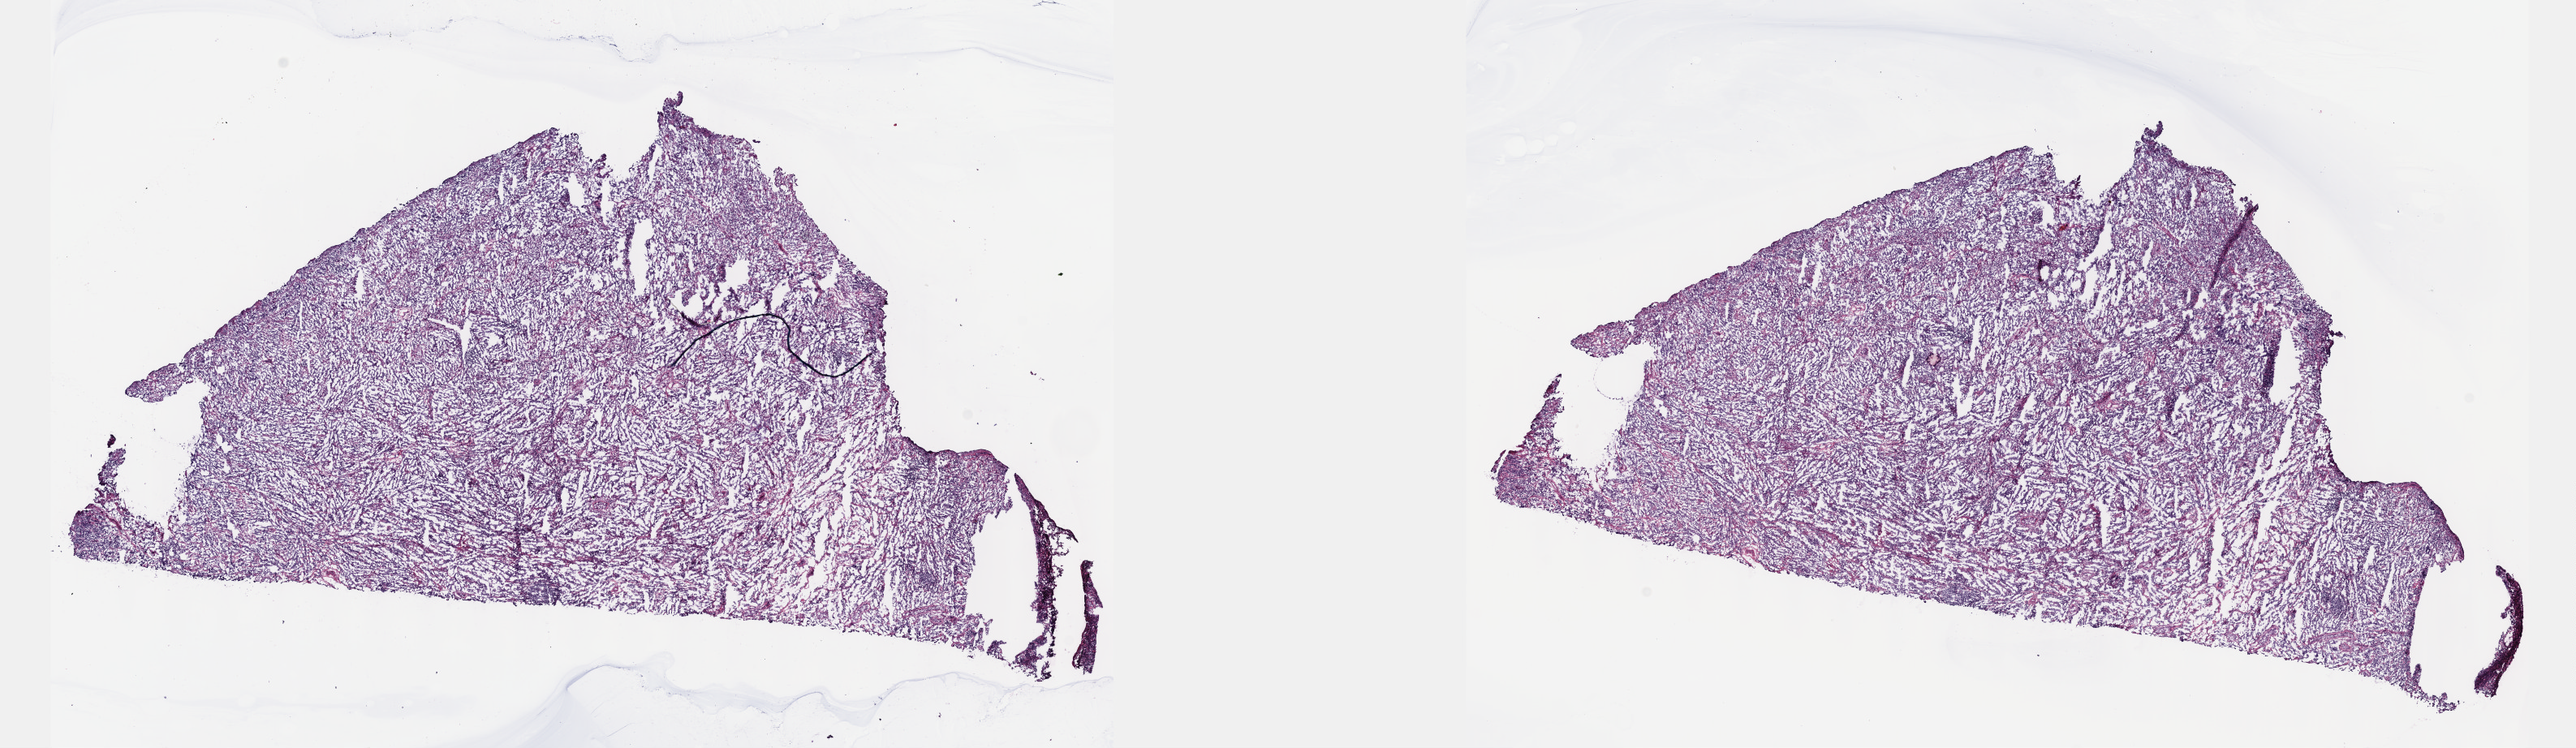
Whole-slide histology image, H&E, a low-resolution overview of the entire scanned area, about 25.7 x 7.5 mm (slide scanned at 40x). Frozen section from the top of the tissue portion. Sample: primary tumour, testis. Patient: male, age at initial diagnosis 23 years. Composition of this section per pathologist review: tumour cells 90%, tumour nuclei 70%, normal cells 0%, stromal cells 10%, necrosis 0%. Inflammatory infiltration, as recorded: lymphocyte infiltration 0%, monocyte infiltration 0%, neutrophil infiltration 0%.
Histologic diagnosis: Seminoma, NOS. Laterality: left. AJCC pathologic stage: IA.